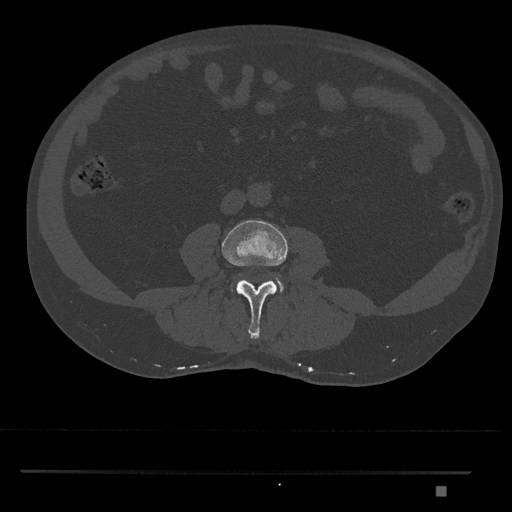
CT including the spine, one axial slice; position 664 of 1134 along the scan axis; reconstruction kernel Br40s/3; bone window (W 1800 / L 400 HU); 0.5 mm slice thickness; 512 × 512 image matrix, field of view 429 × 429 mm. Patient: male, 65 years. Case-level facts recorded for this patient, not image findings: primary cancer: prostate.
Outlined on this slice (semi-automatically segmented with operator editing):
- L3 vertebra: box from (x=222, y=220) to (x=288, y=339) px
- L4 vertebra: (x=276, y=277)–(x=284, y=291)